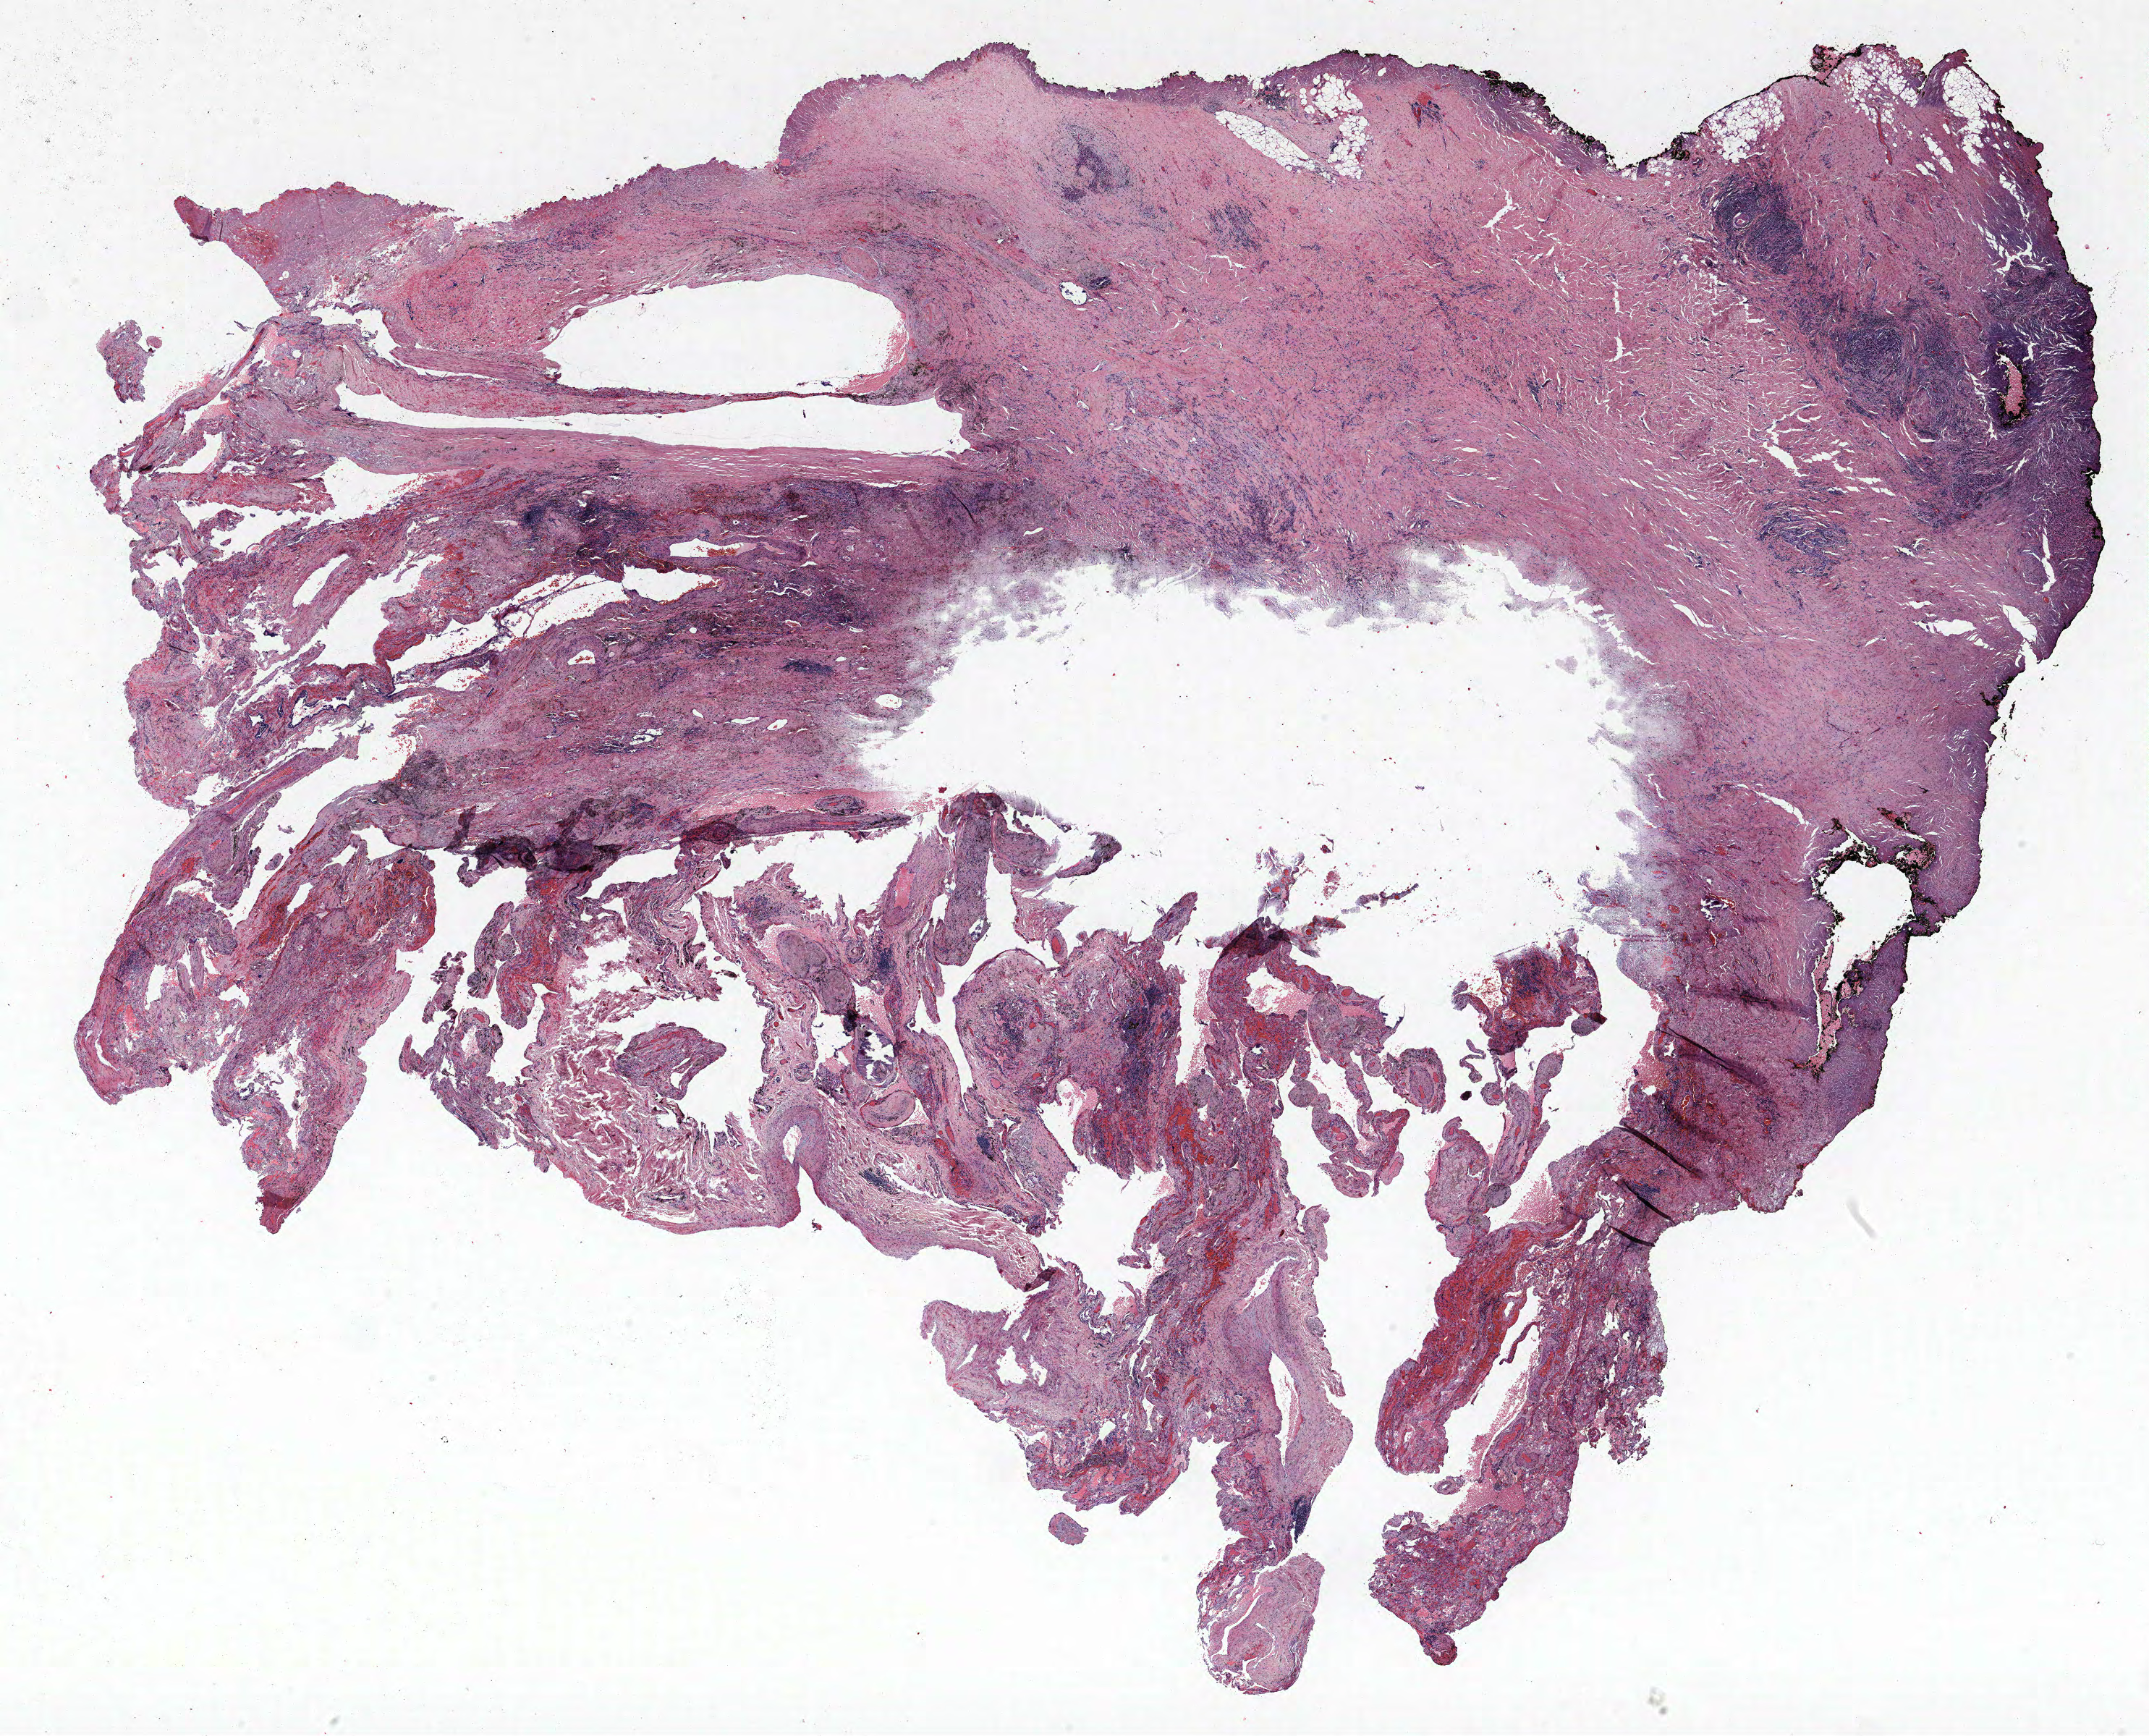
Whole-slide histology image, Hematoxylin and eosin (H&E) stained, shown as a low-resolution overview of the whole scanned area (about 23.8 x 19.2 mm, slide scanned at 40x). Formalin-fixed paraffin-embedded (FFPE) section. Lung tissue. Male patient, aged 65 at enrolment. Current smoker at enrolment. Grade: poorly differentiated (G3).
Participant's lung-cancer diagnosis: Adenocarcinoma, NOS (ICD-O-3 8140/3). Stage (AJCC 6th edition): IB. Primary tumour location (clinical record): right upper lobe. Tumour size (pathology): 13 mm. Note: participant had 2 primary lung cancers recorded; fields above describe the first.